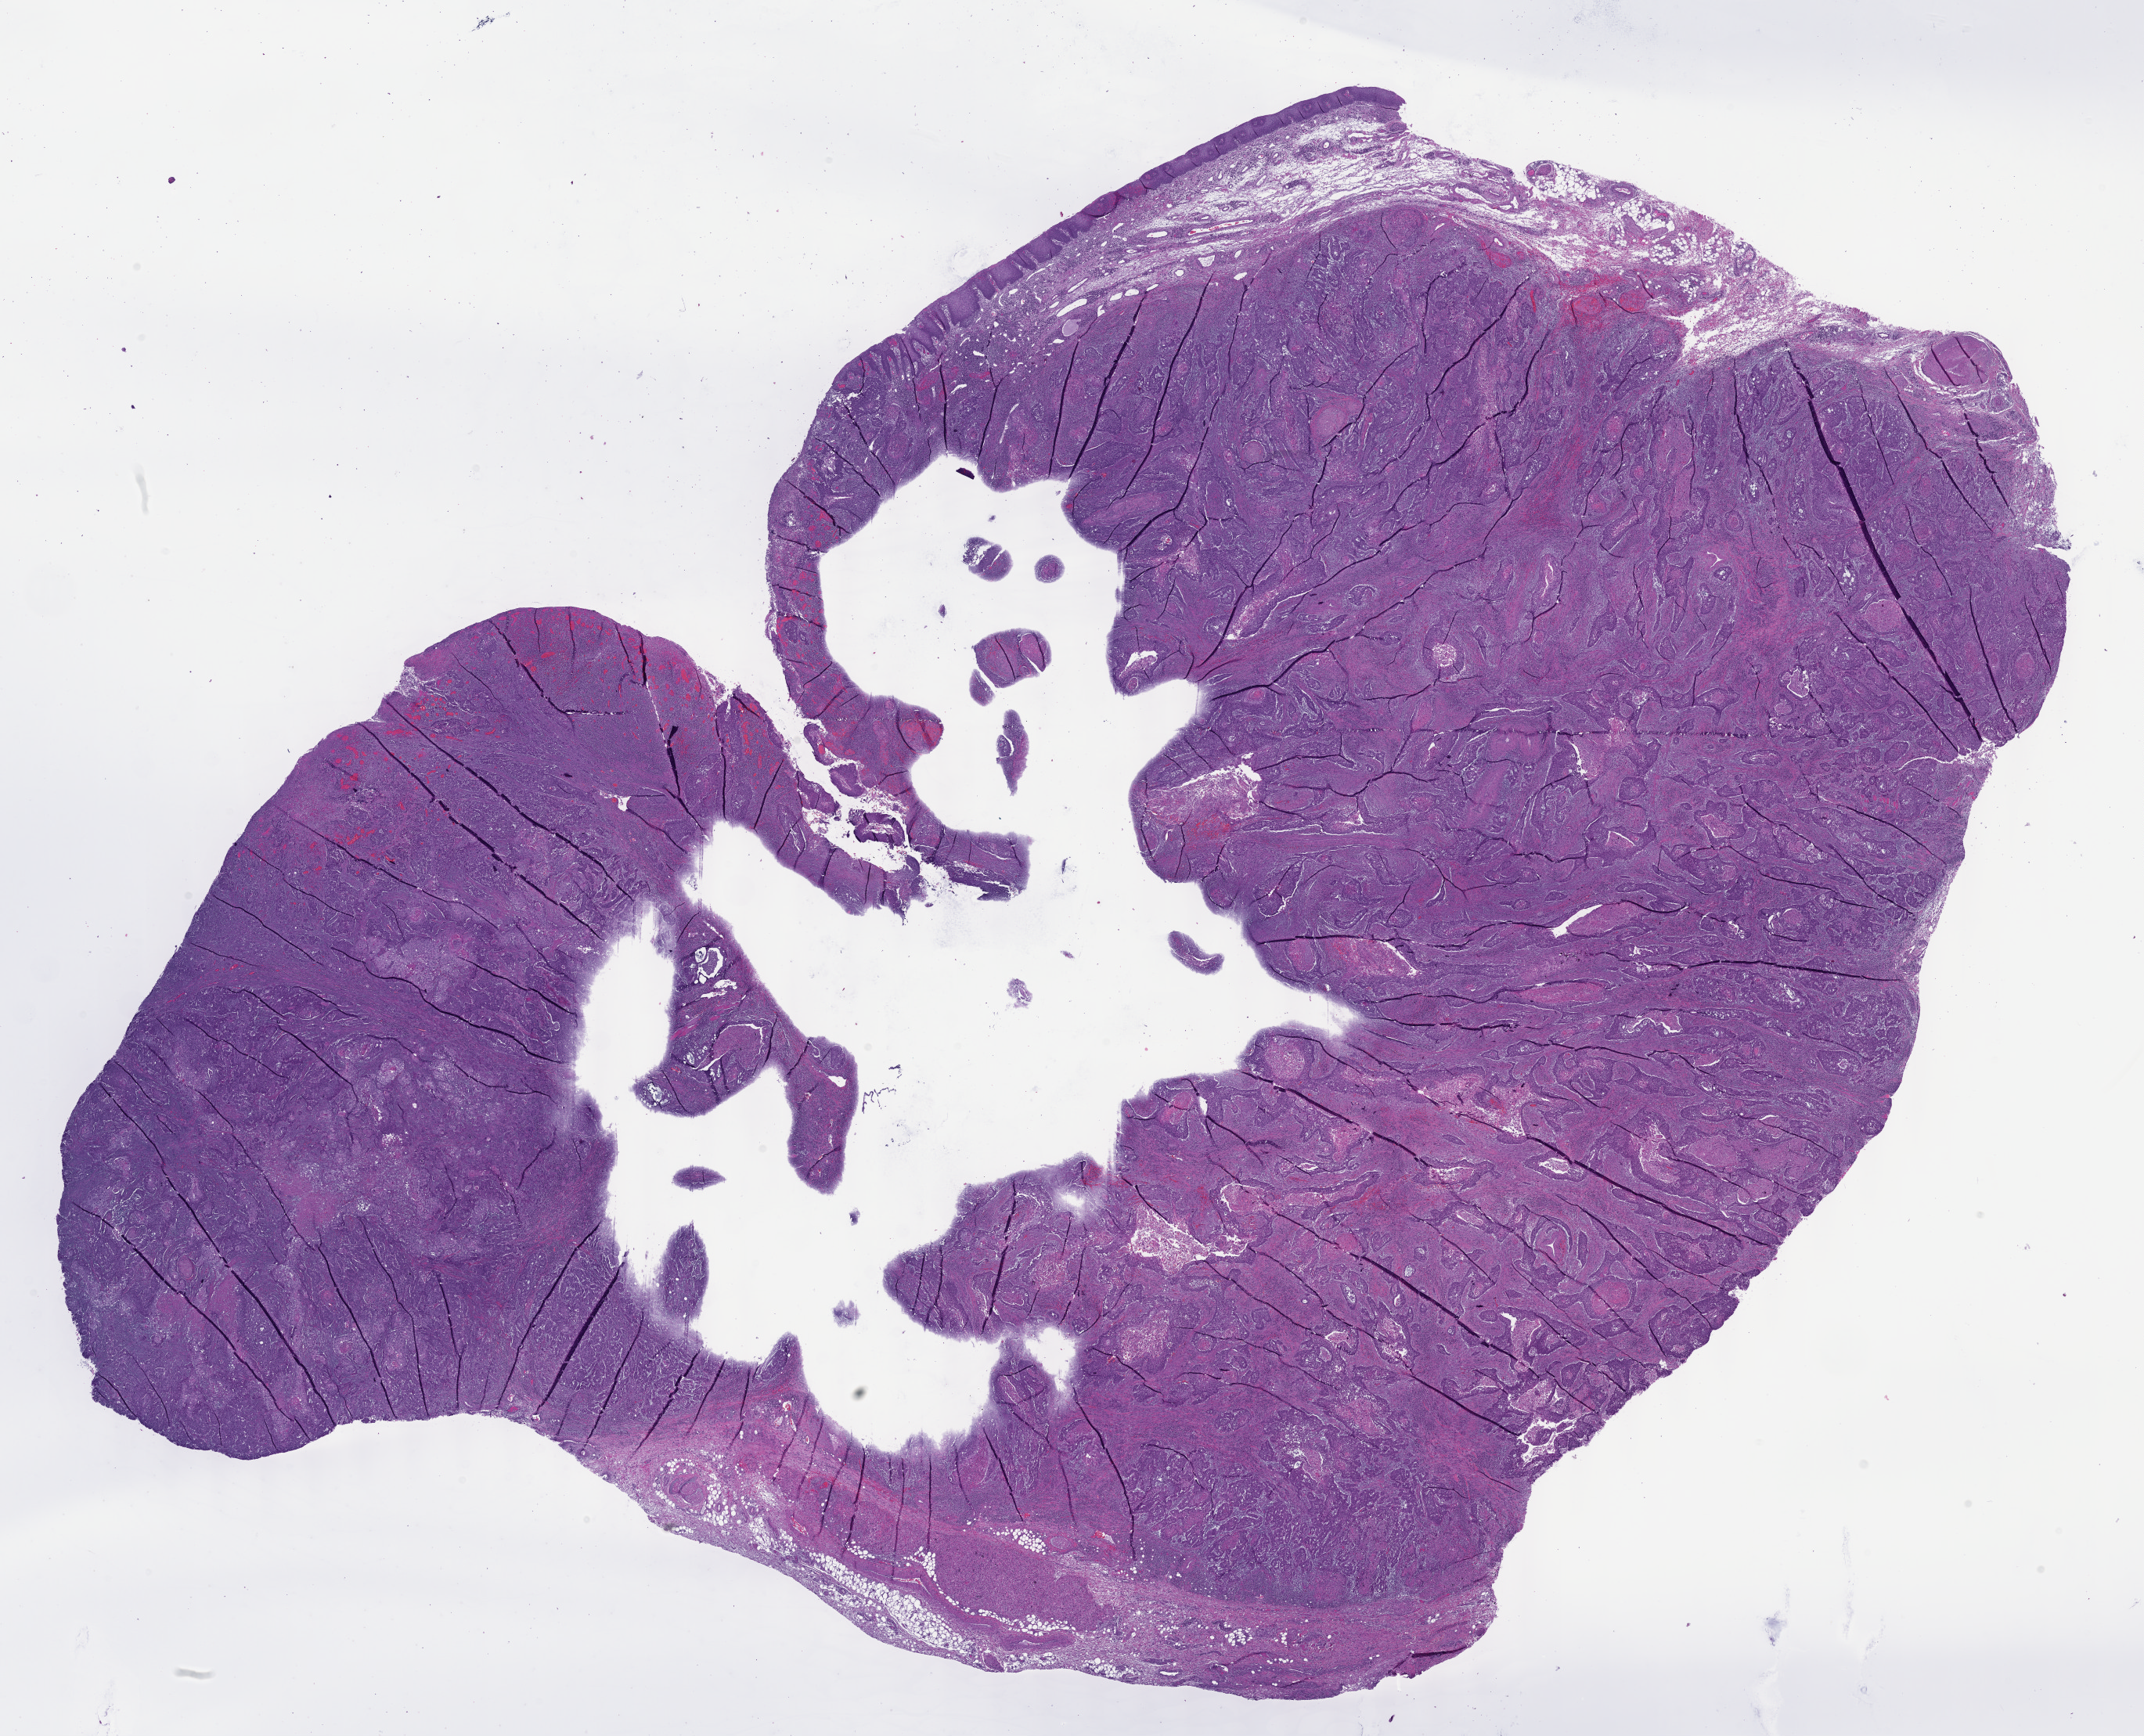
Digitized H&E tissue section (whole slide) — shown as a low-resolution overview of the whole scanned area (about 22.1 x 17.9 mm, from a 40x scan), formalin-fixed paraffin-embedded (FFPE) diagnostic section, primary tumour sample from the head and neck. Male, age 52 years at initial diagnosis. Histologic grade: G3 (poorly differentiated).
- AJCC pathologic stage: IVA (7th edition)
- lymph nodes positive (case pathology): 42 of 47 examined
- diagnosis: Squamous cell carcinoma, NOS (larynx, NOS)